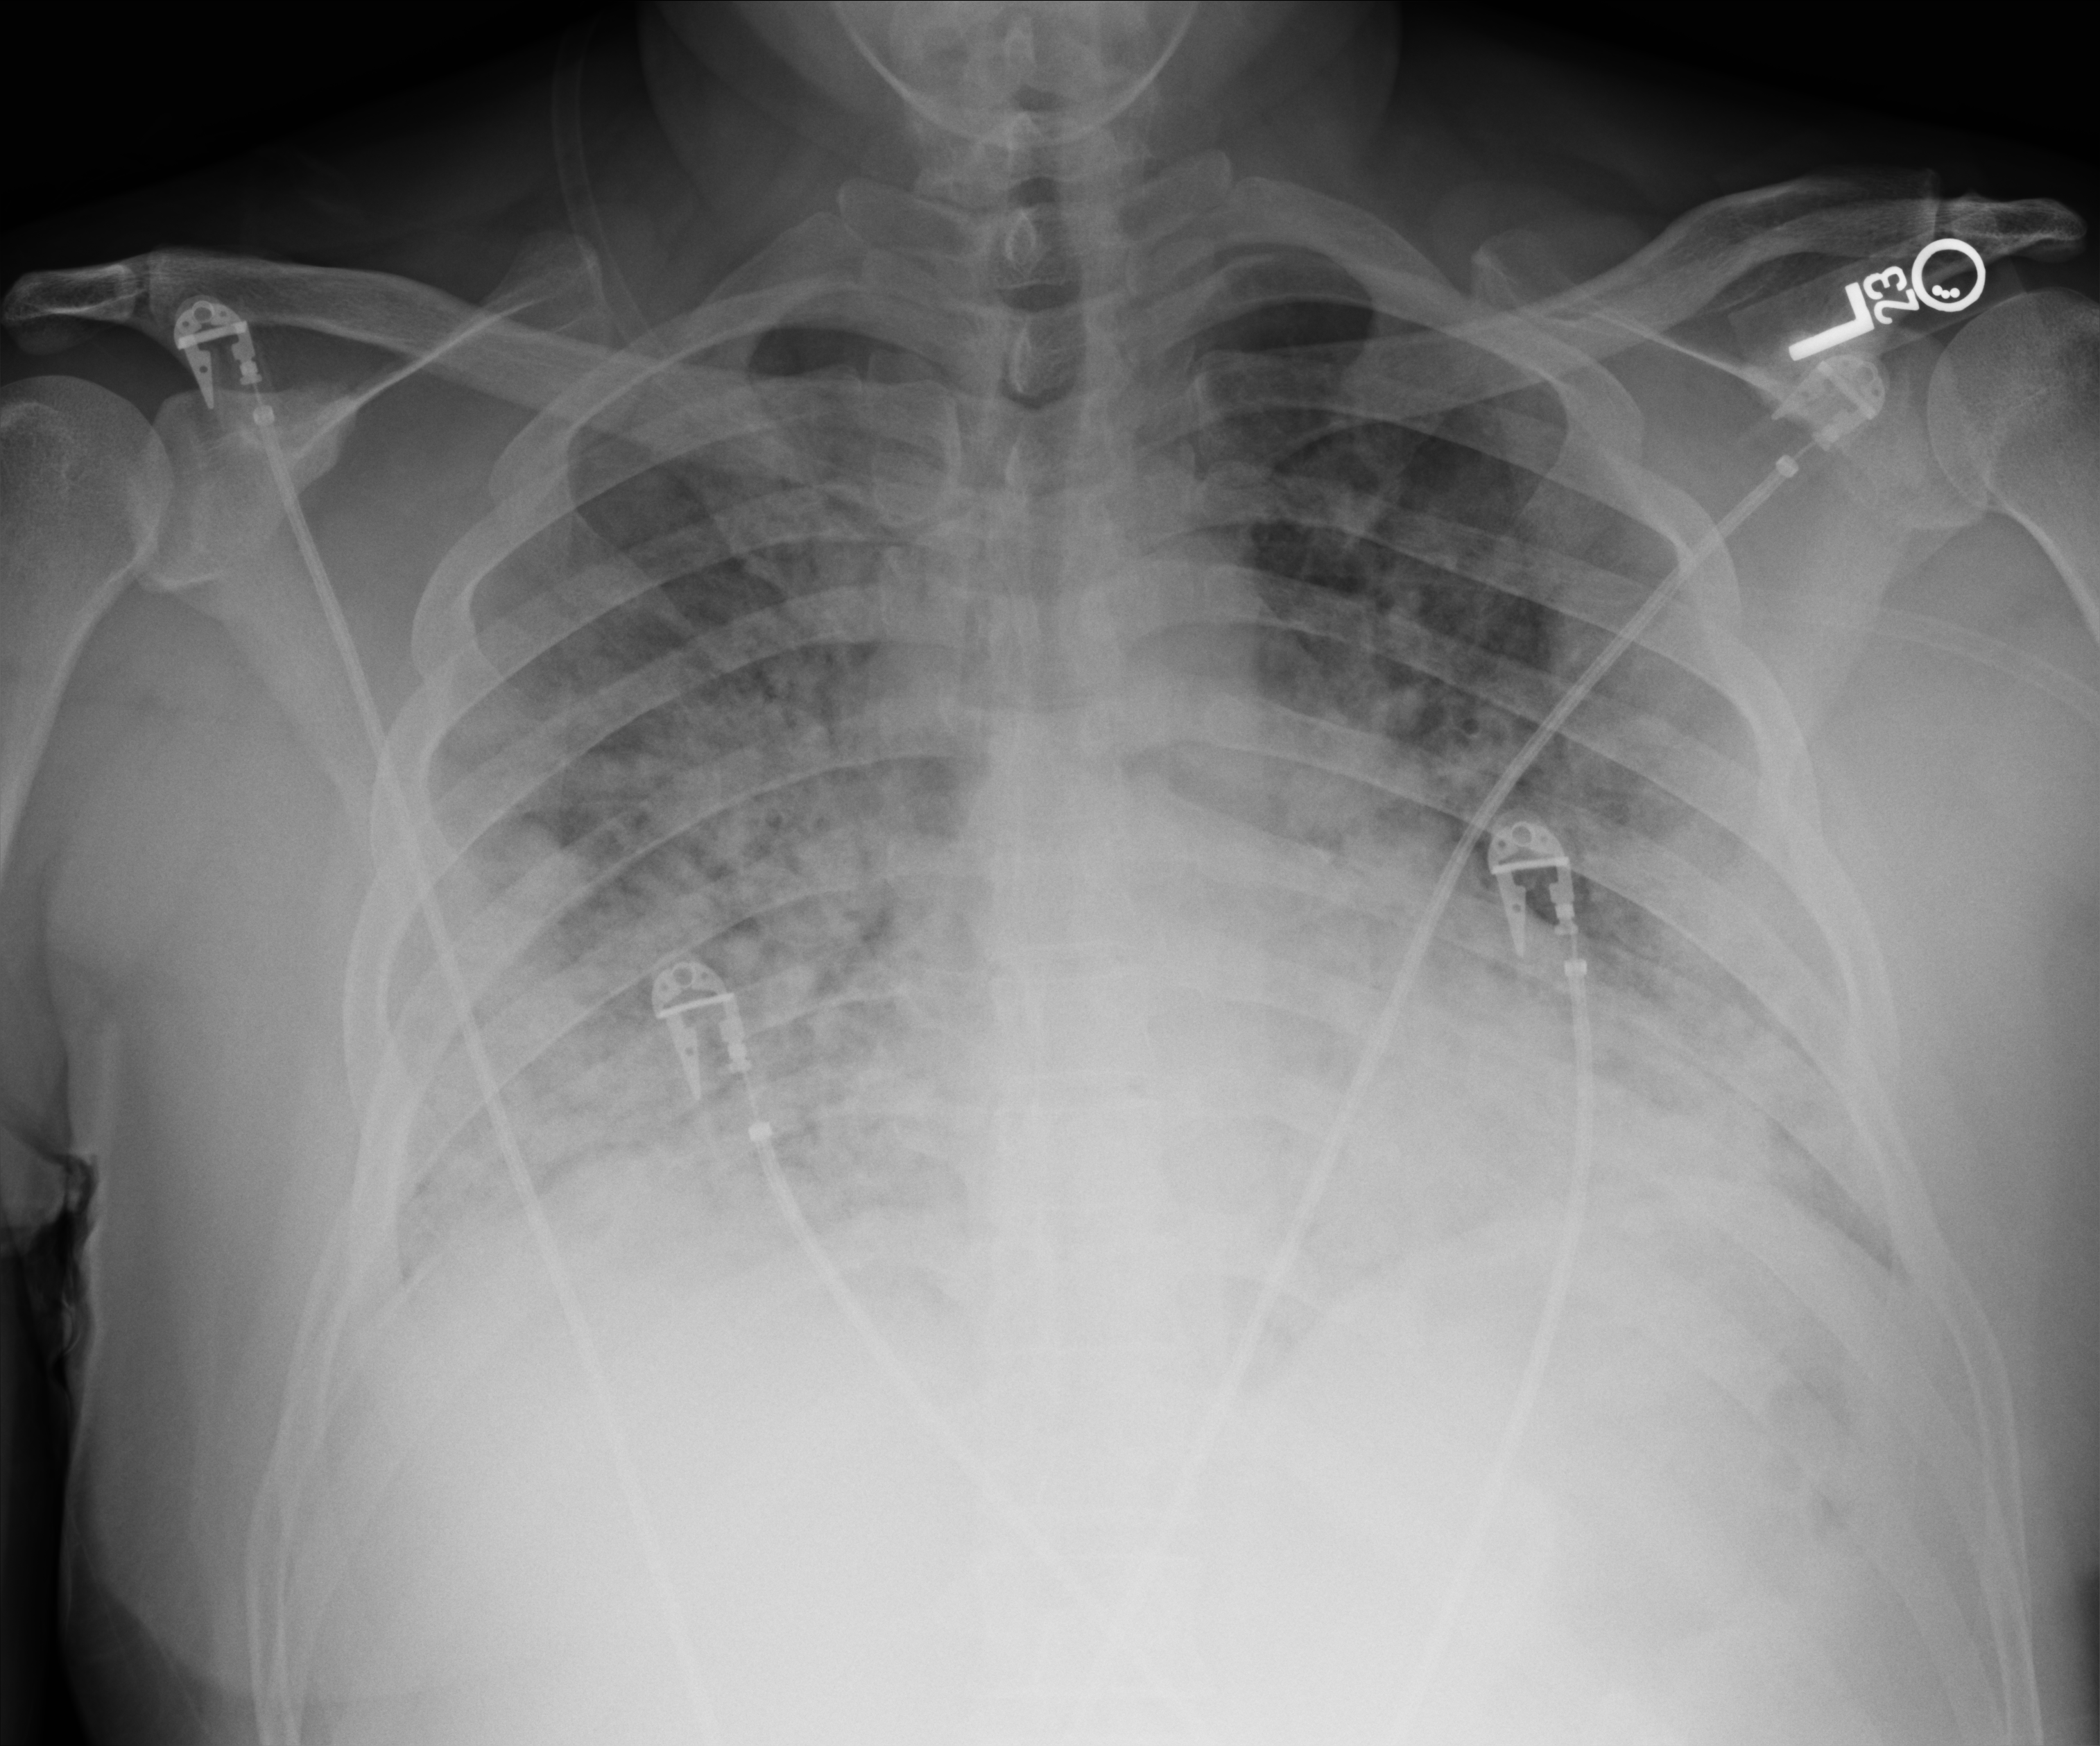
Bedside chest radiograph (computed radiography), anteroposterior (AP) projection. Patient hospitalised with COVID-19; male, aged 18–59 years.
From the hospital-stay record, not from the radiograph (when in the stay this image was taken is not recorded):
- length of hospital stay: 26 days